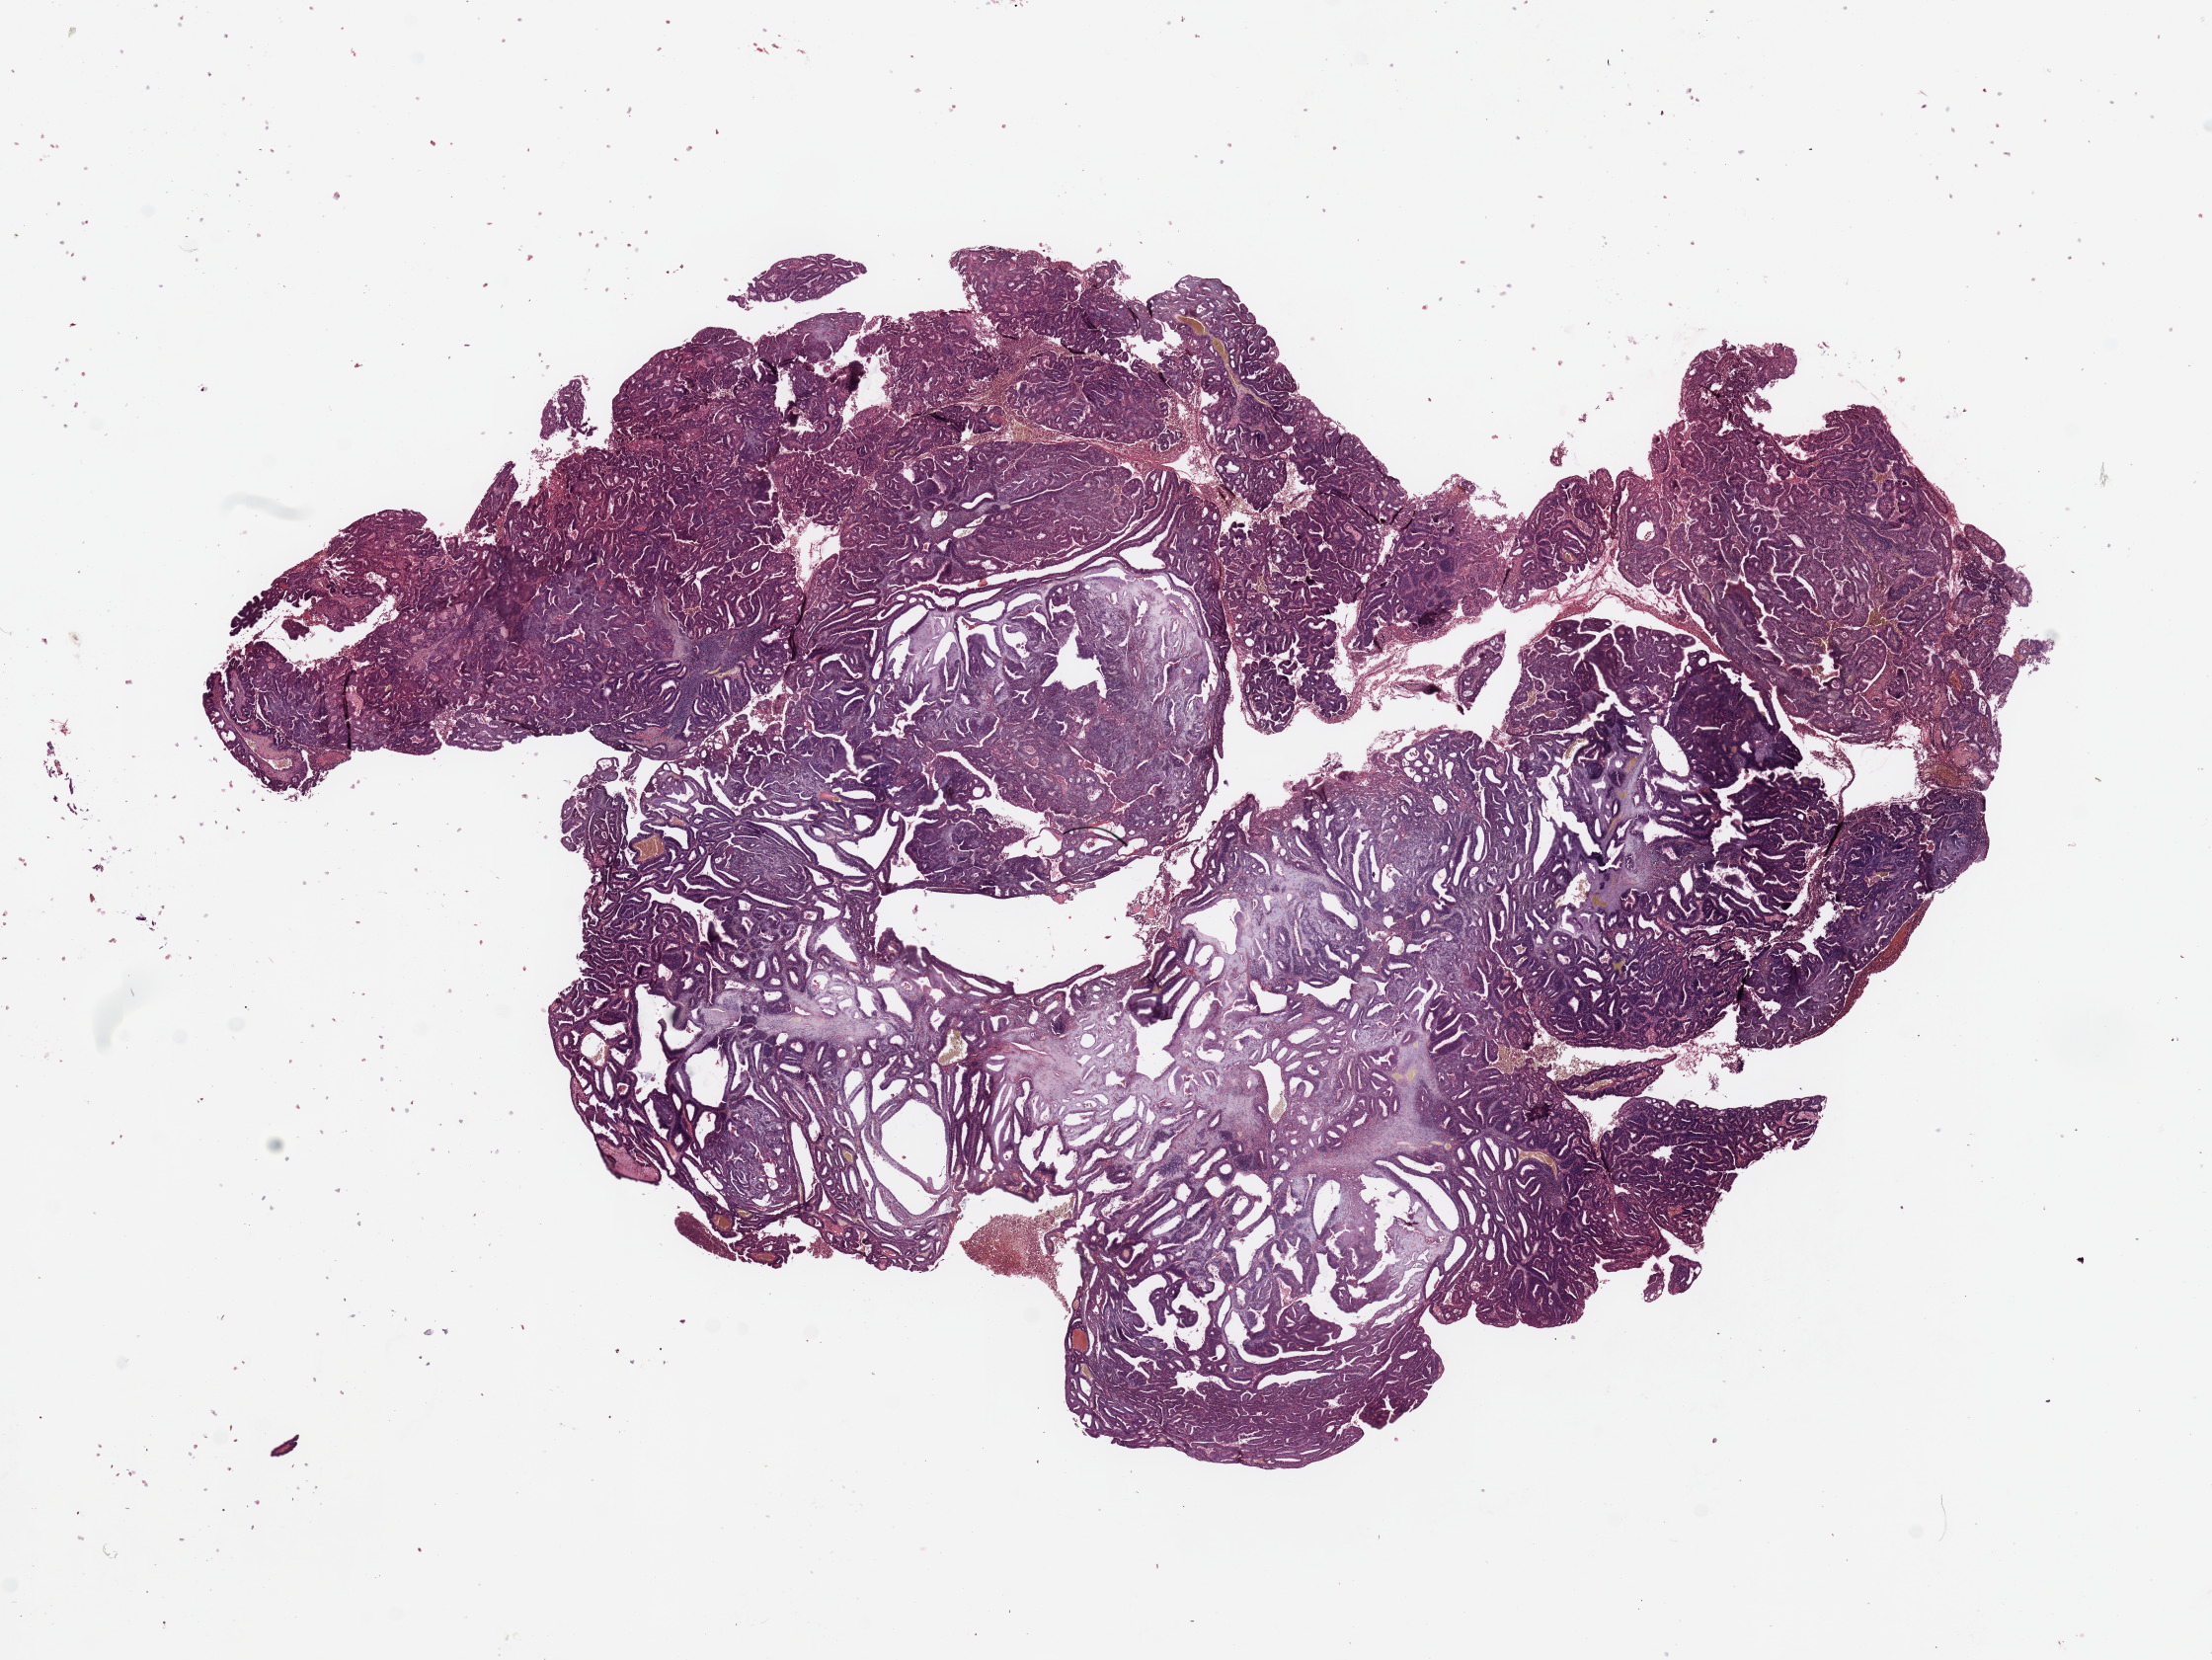
H&E-stained whole-slide image, whole scanned area (about 17.7 x 13.3 mm) shown as a low-resolution overview. Uterus, tissue type not recorded.
- patient diagnosis (cohort enrolment): corpus endometrial carcinoma (uterus)